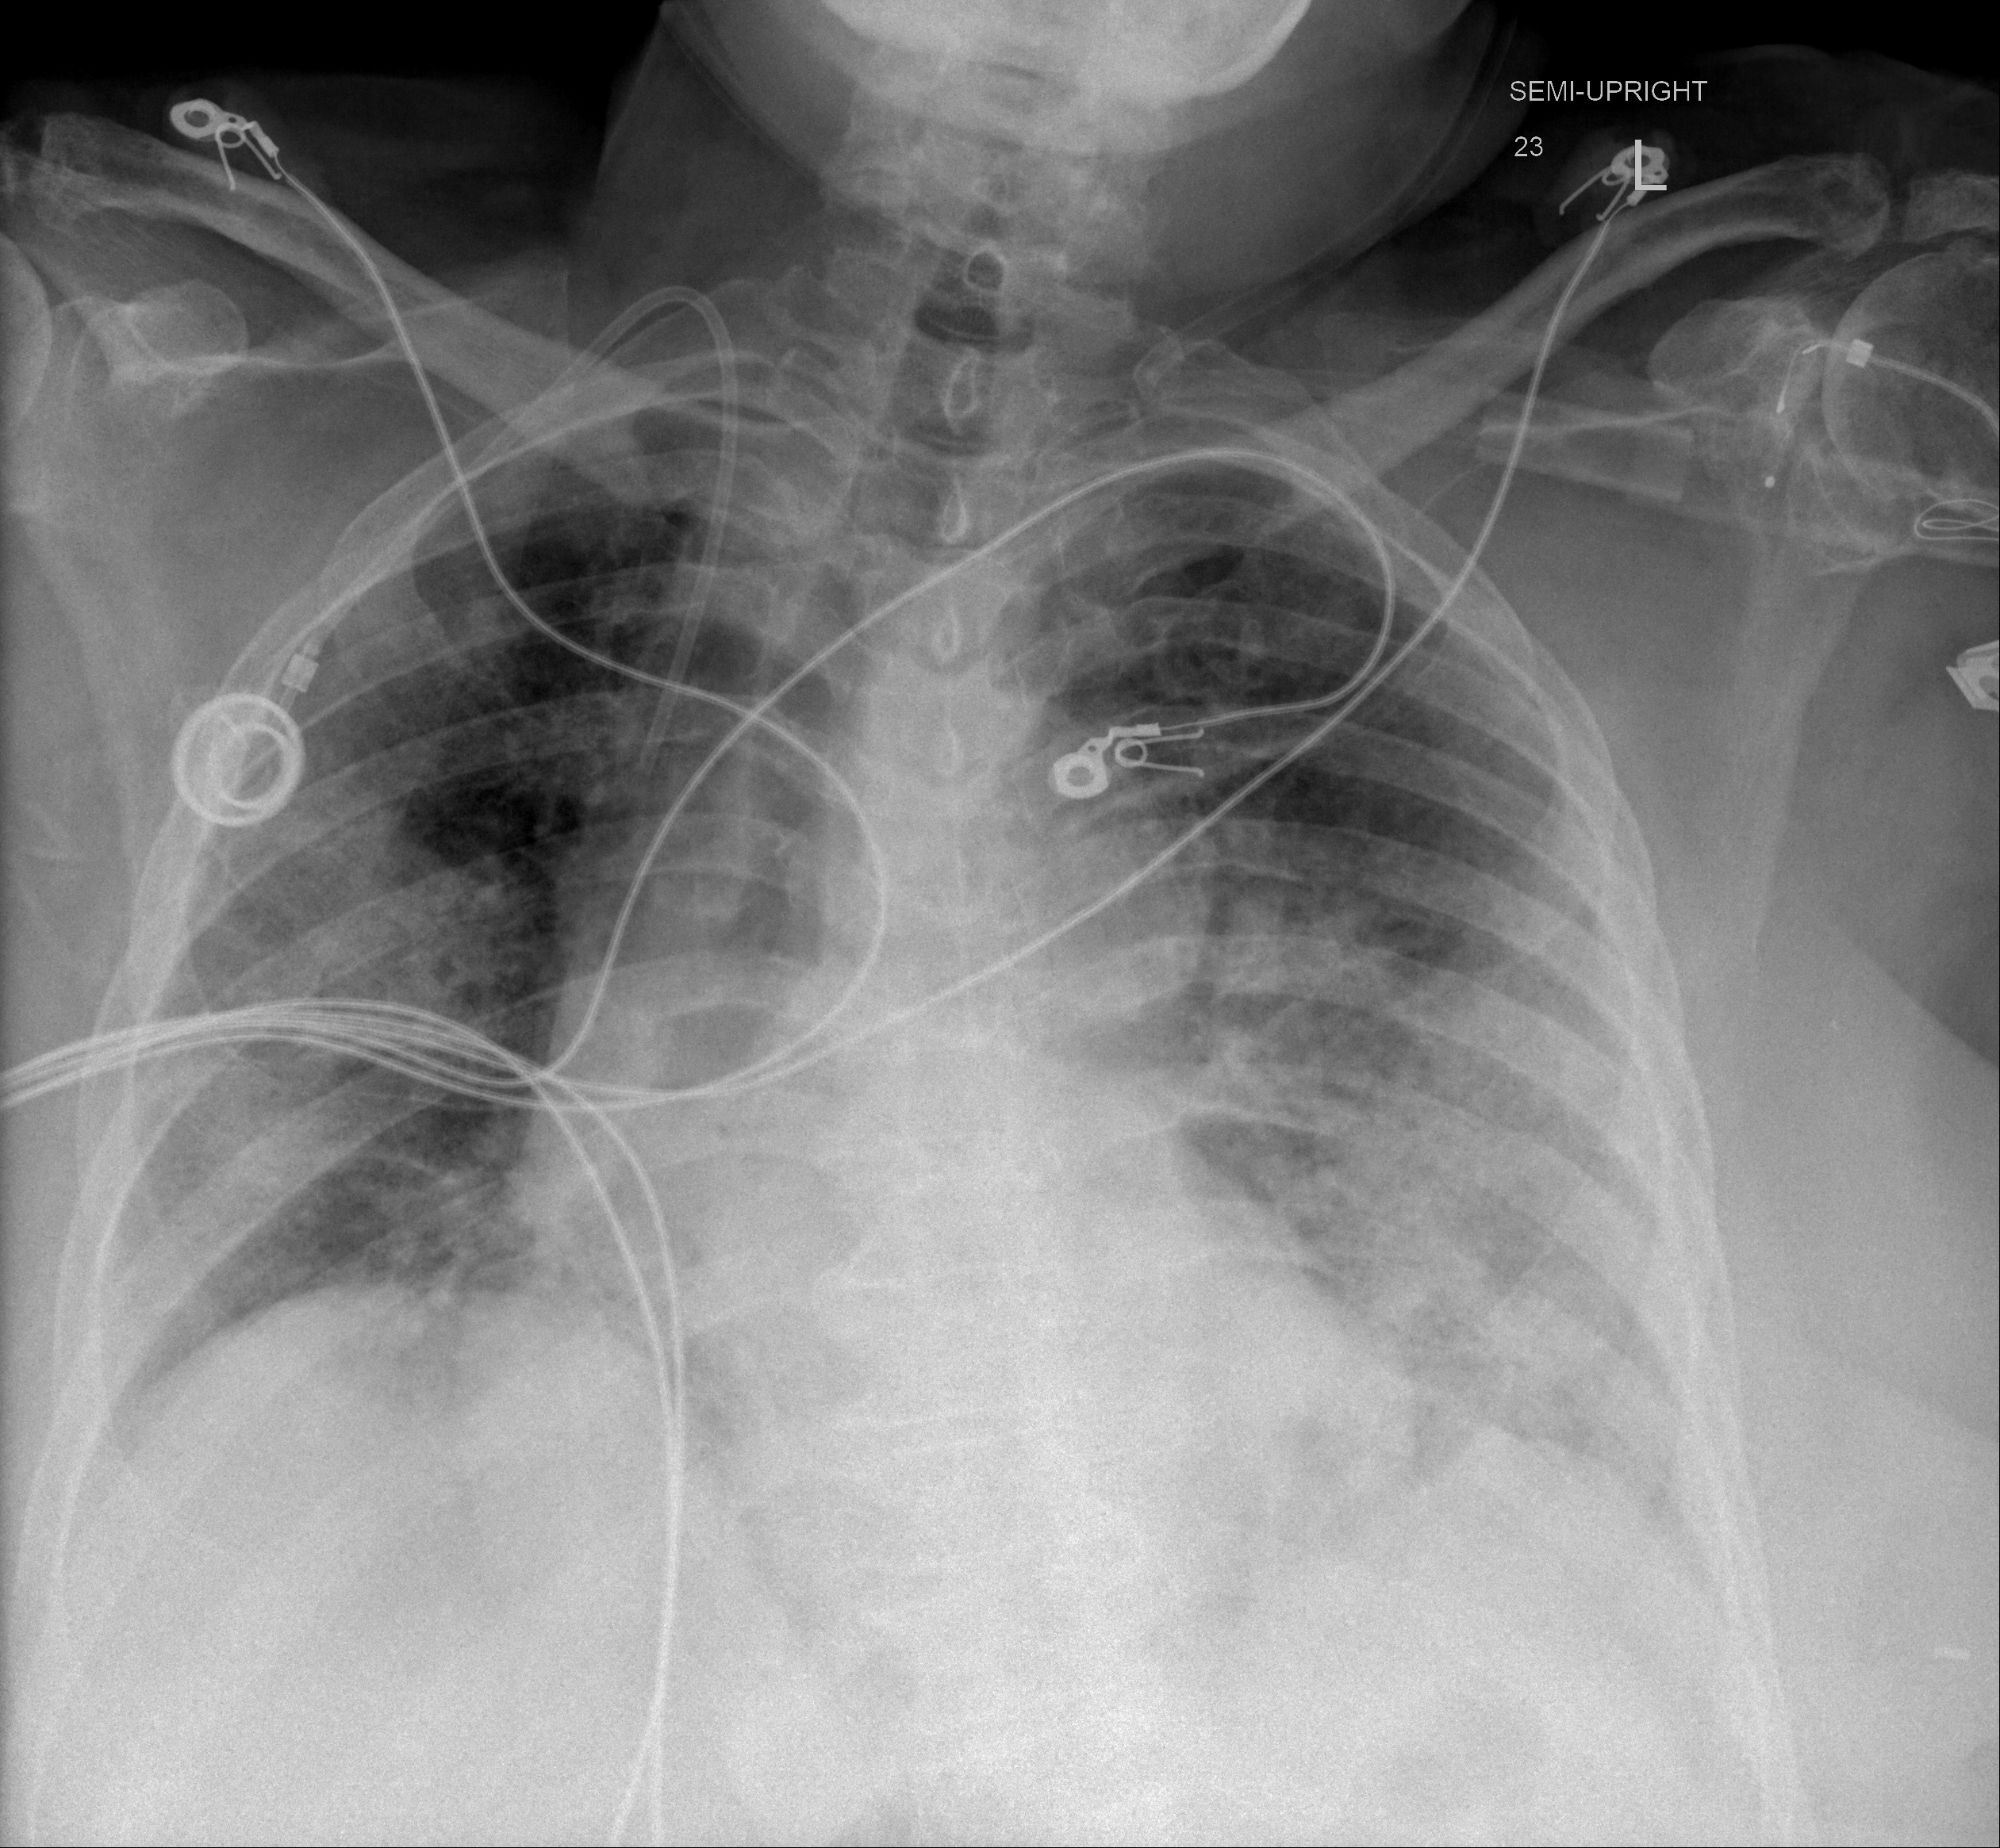
Chest X-ray (portable), AP projection. Female patient, age 76 years; COVID-19 (test-positive).
Radiologist key findings (as recorded): Slight increase of the ill-defined hazy airspace opacifications throughout the bilateral lungs with subtle lower lobe predominance.